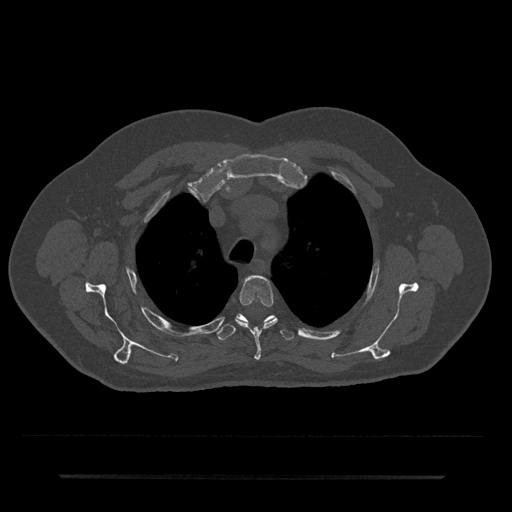
CT including the spine, one axial slice. Slice 555 of 797 in the series (ordered by position). Reconstruction kernel Br40s/3. Bone window (W 1800 / L 400 HU). 0.5 mm slice thickness. 512 × 512 image matrix. Patient: male, 69 years. Case-level facts recorded for this patient, not image findings: primary cancer: prostate.
Annotated regions visible in this slice (semi-automatic segmentation, software-assisted and operator-edited):
- T3 vertebra: bounding box (x1, y1, x2, y2) in pixels: (236, 276, 278, 360)
- T4 vertebra: (217, 314, 294, 340)